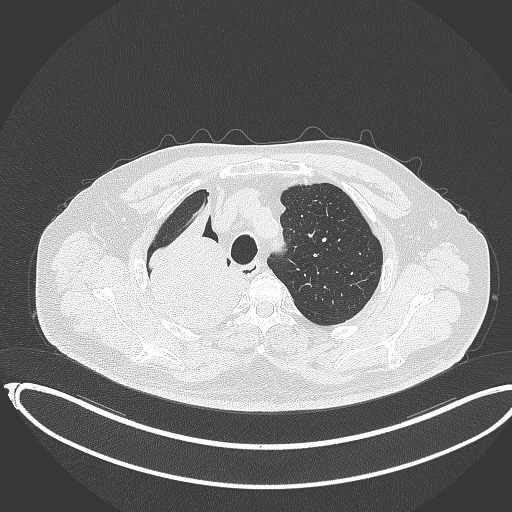
Chest CT, one axial slice; slice 295 of 403 in the series (ordered by position); reconstruction kernel B70f; 120 kVp; lung window (W 1500 / L -600 HU); 1 mm slice thickness; 512 × 512 image matrix, field of view 436 × 436 mm. Patient: male, 68 years. From the clinical record (not read from this slice): clinical TNM (as recorded): T2a N0 M0.
Outlined on this slice (rectangle marked by the reading radiologist):
- lung tumour (recorded histology: adenocarcinoma): bounding box <135,194,247,329> (left, top, right, bottom; pixels)